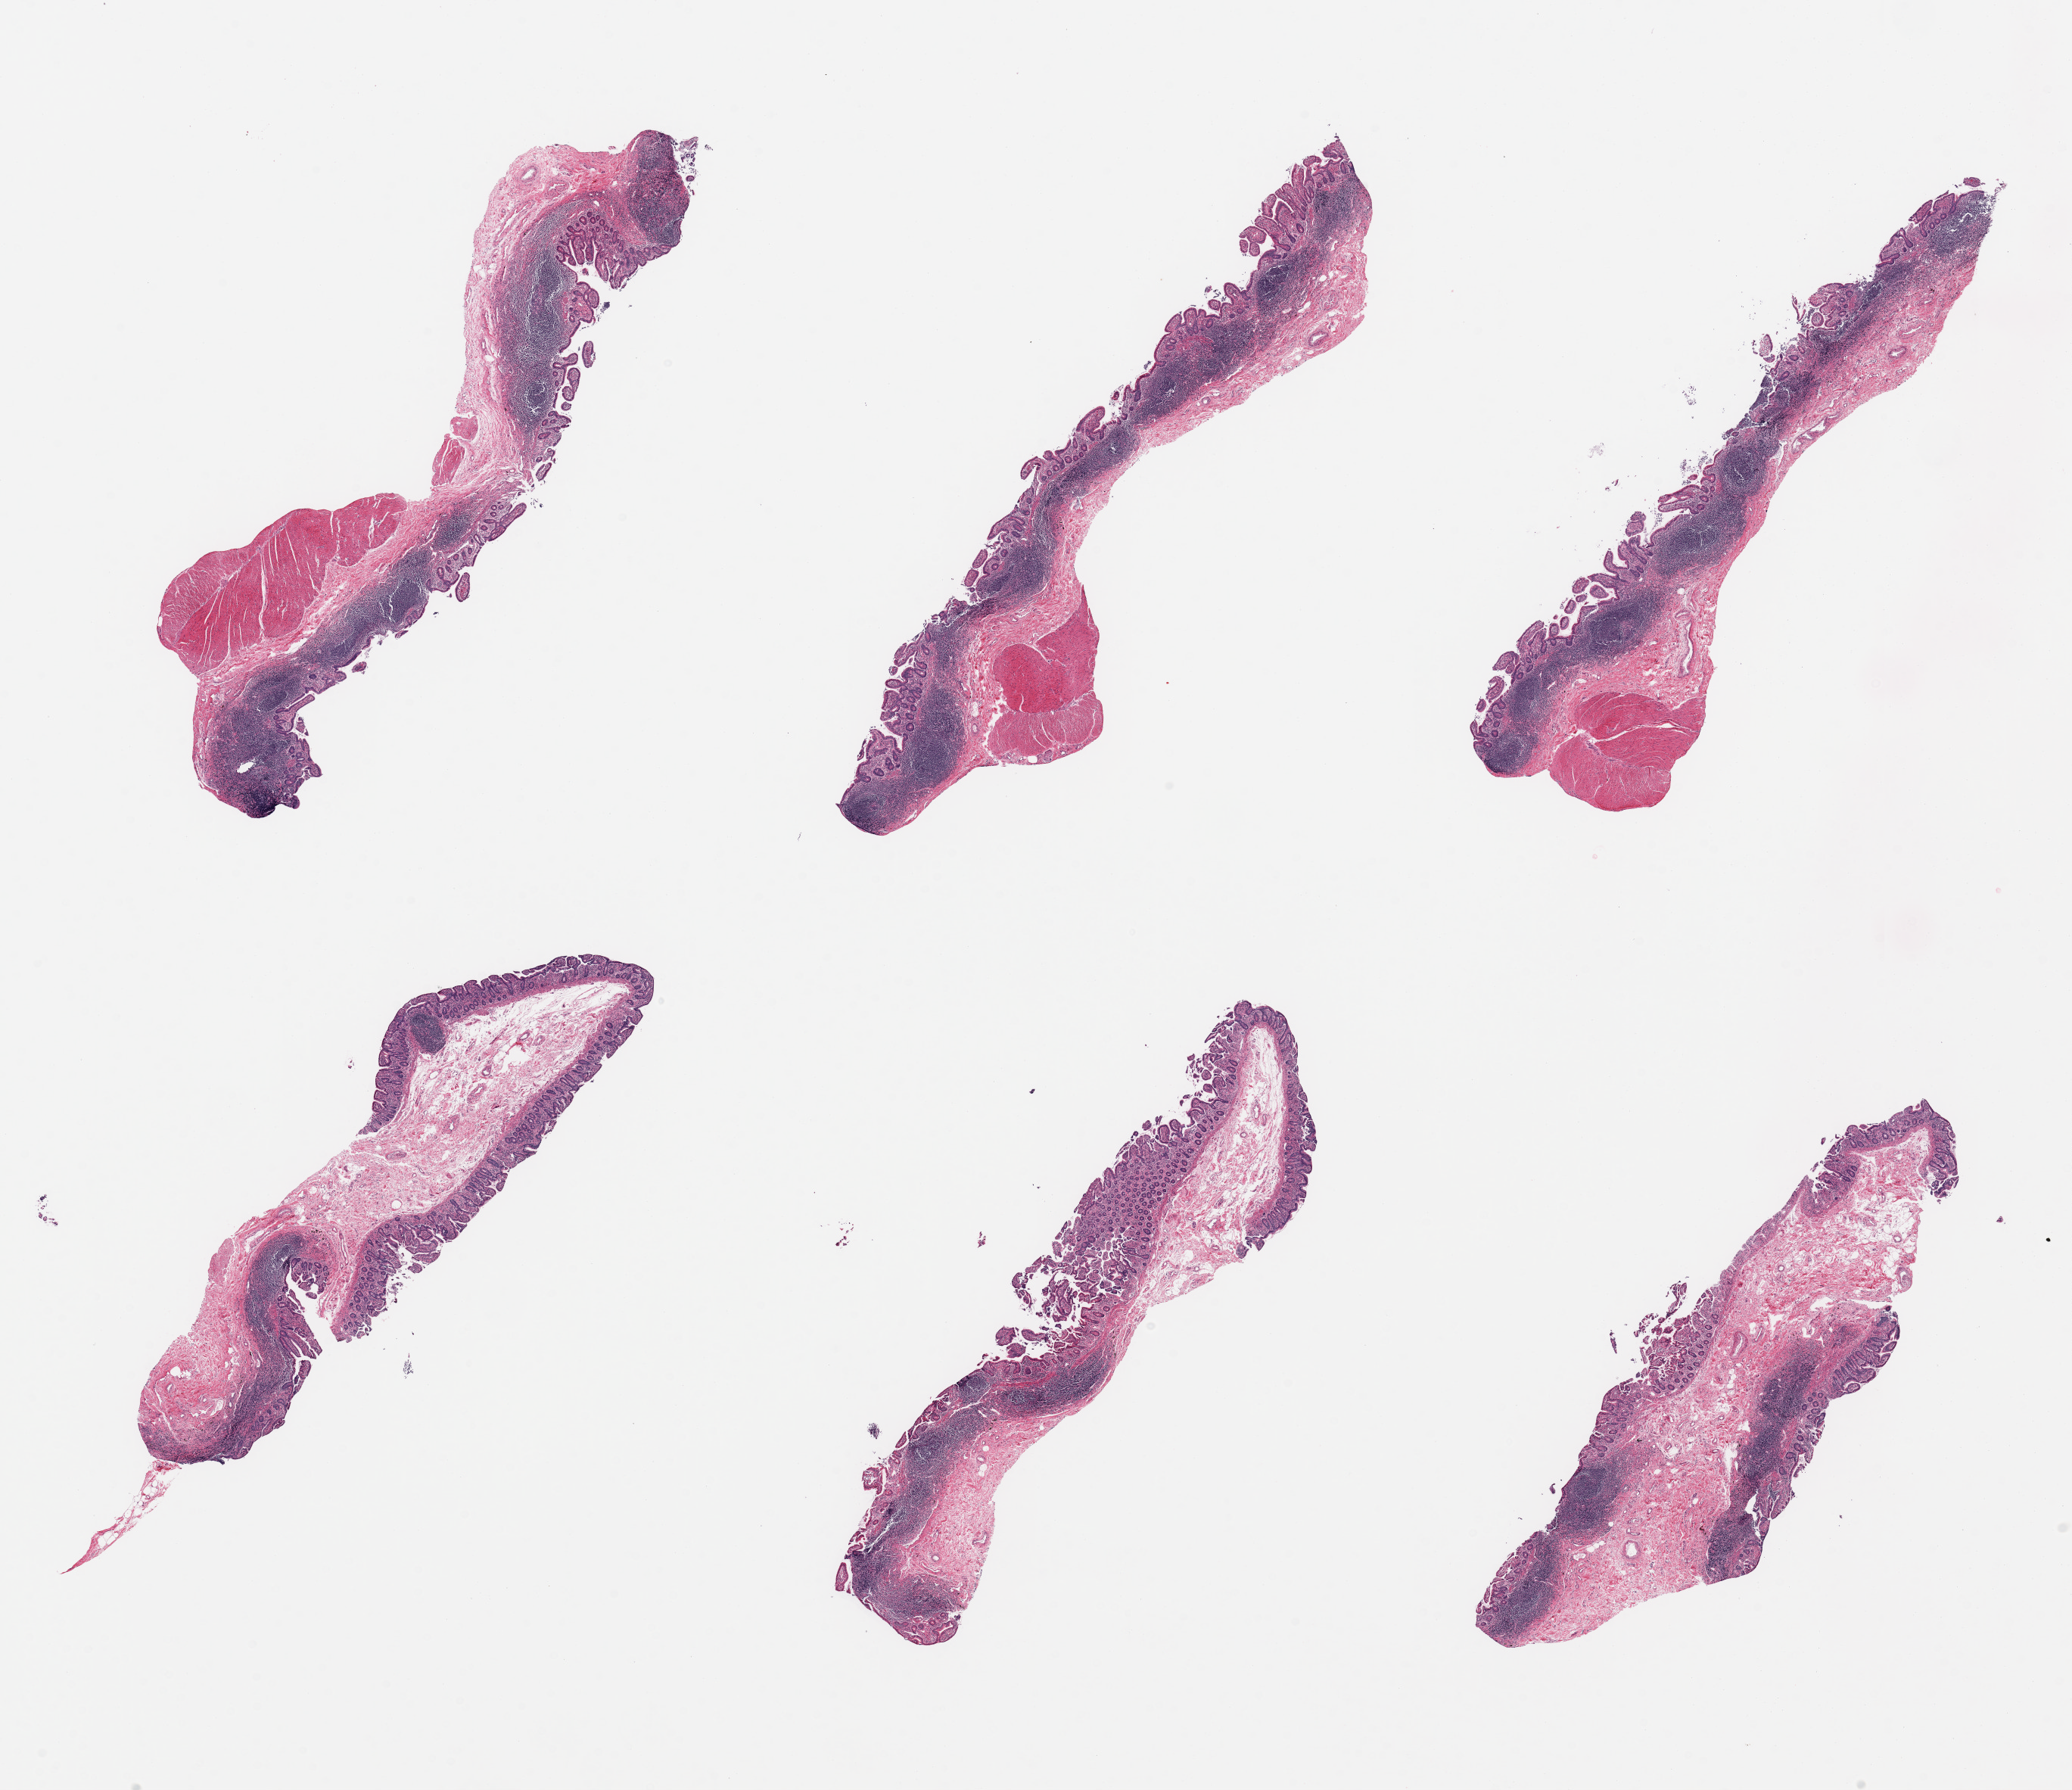
H&E whole-slide image, whole scanned area (about 21.7 x 18.7 mm, from a 20x scan) shown as a low-resolution overview; PAXgene-fixed paraffin-embedded (PFPE) section; target tissue: ileum; donor tissue sample.
Reviewer comment on this tissue sample: 6 pieces; good lymphoid component, small portion of residual muscularis in 3 of 6 pieces.